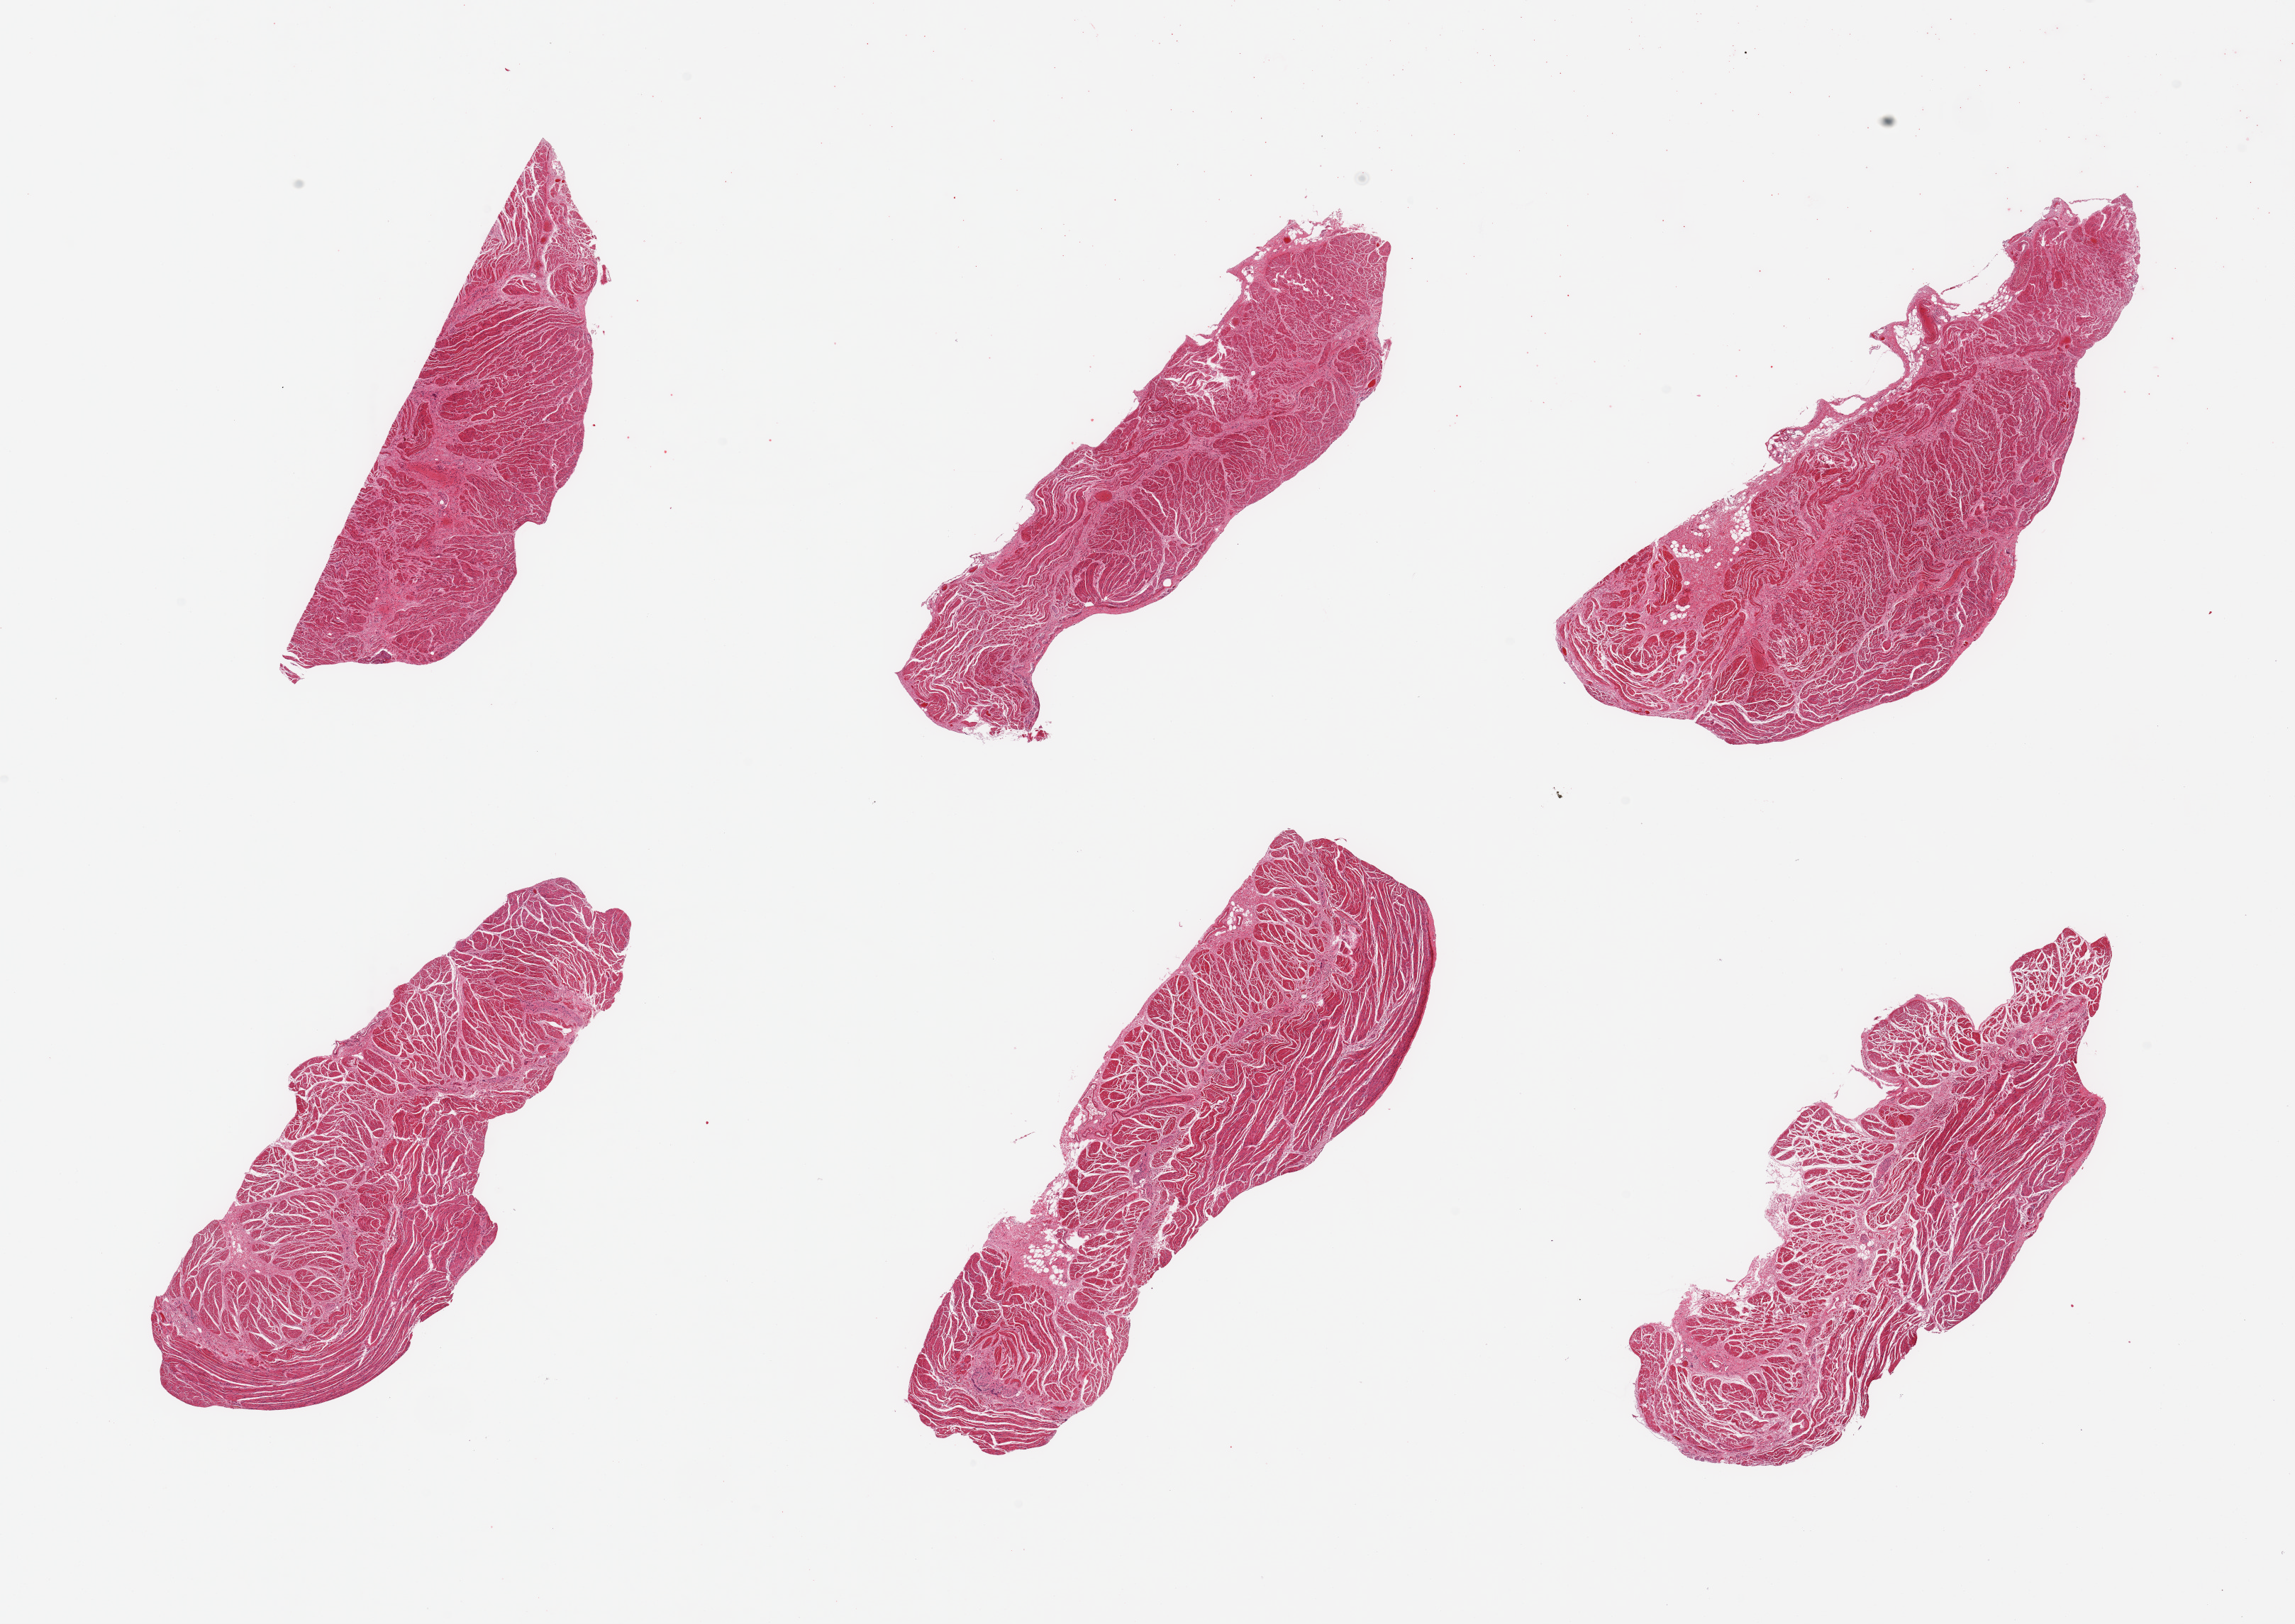
Whole-slide image, H&E stain, brightfield, a low-resolution overview of the entire scanned area, about 25.6 x 18.1 mm (acquisition: 20x scan). PAXgene-fixed paraffin-embedded (PFPE) section. Section of esophageal muscle (target tissue). Tissue donor sample. Donor sex: male.
Review note (as recorded): 6 pieces, confirmed target muscularis.